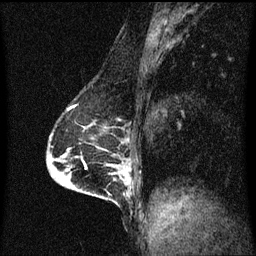
Breast MRI (dynamic contrast-enhanced), one sagittal slice; slice 32 of 60 in the series (ordered by position); dynamic contrast-enhanced series, image 2 of 3 at this slice position (ordered by acquisition); 1.5 T; TE 4.2 ms, TR 8.4 ms; 2 mm slice thickness; 256 × 256 image matrix, field of view 200 × 200 mm. Patient: female, 64 years.
Annotated regions visible in this slice (semi-automatic segmentation, software-assisted and operator-edited):
- analysis volume of interest (the breast-tissue region the enhancement analysis was run in; not a lesion): bounding box [x1, y1, x2, y2] px = [90, 164, 129, 203]
- tumour enhancement mask (voxels above the 70 % enhancement threshold inside the analysis volume of interest): [96, 166, 113, 195]